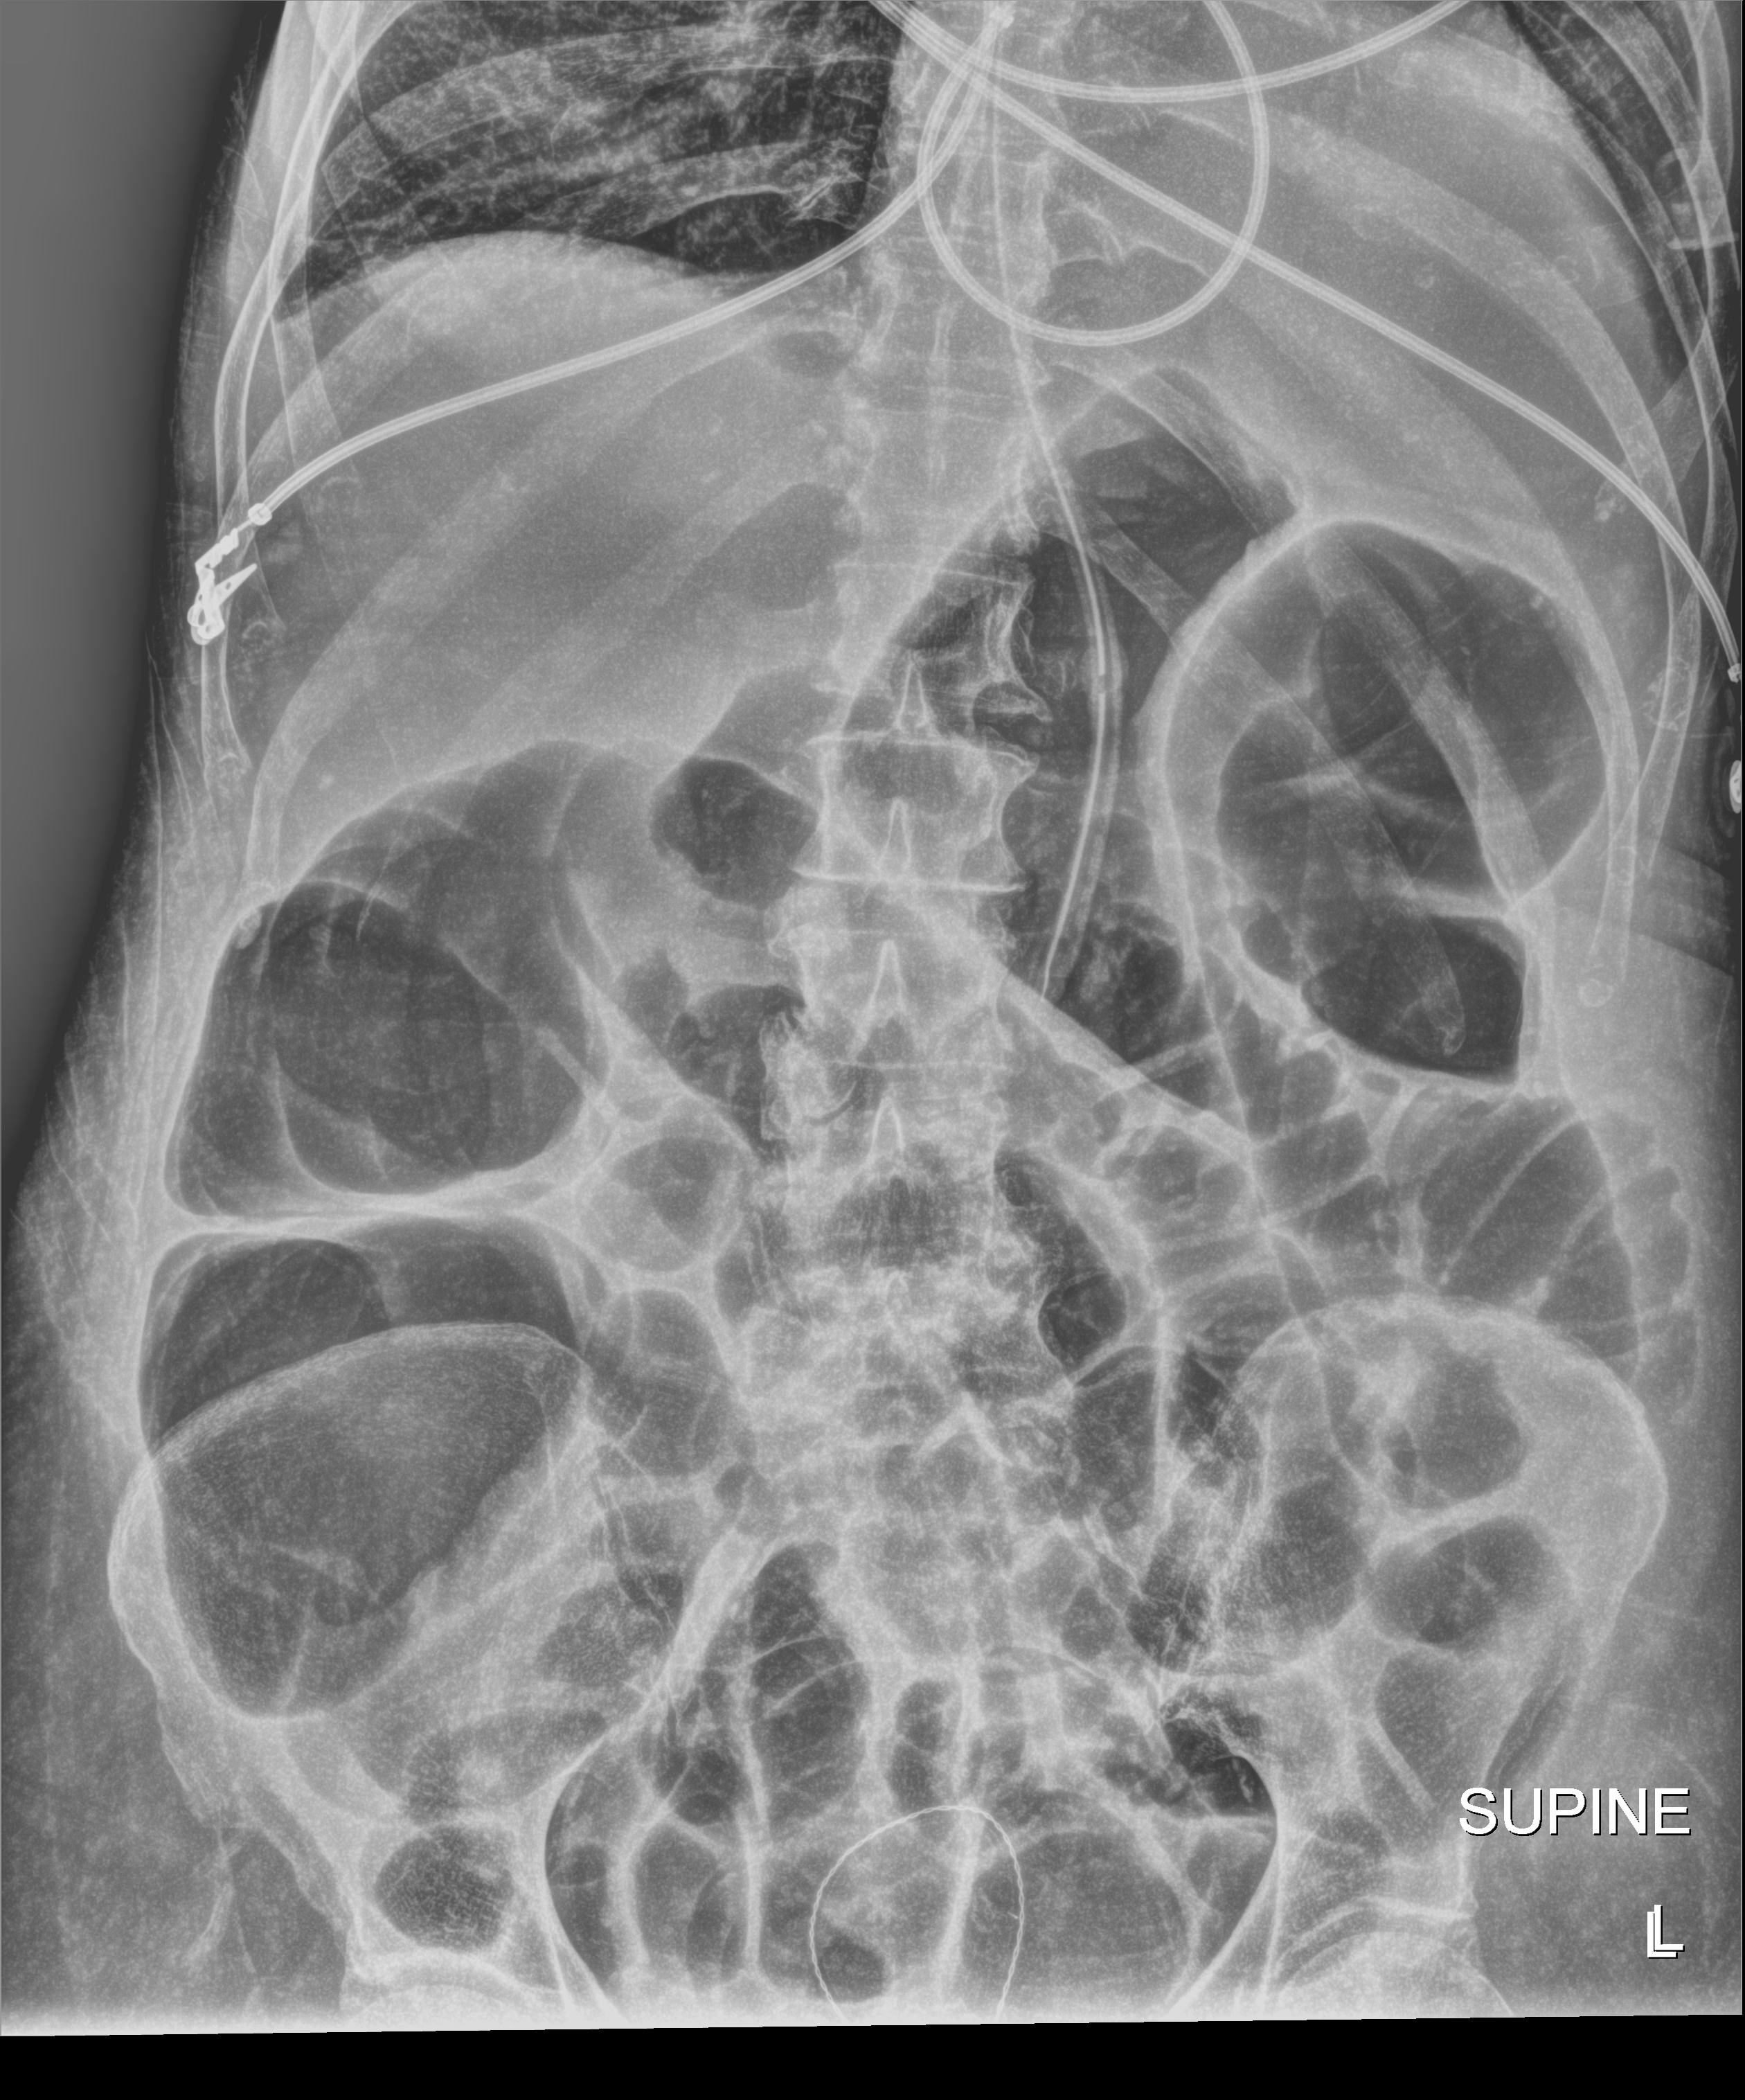
Portable abdomen radiograph; anteroposterior (AP) projection. Patient hospitalised with COVID-19; female, aged 60–74 years.
From the hospital-stay record, not from the radiograph (when in the stay this image was taken is not recorded): mechanically ventilated during this hospital stay: yes; length of hospital stay: 38 days.